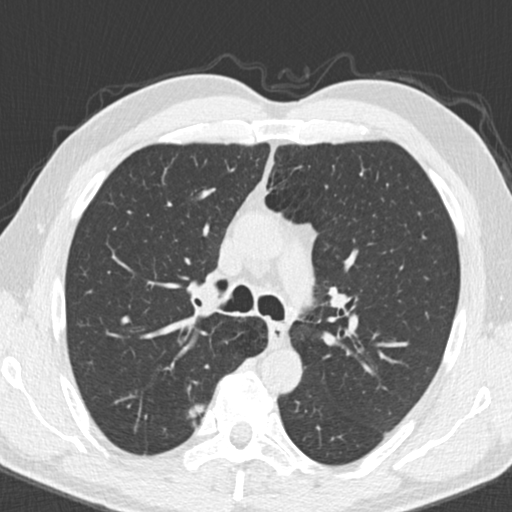
Axial slice from a low-dose chest CT screening exam; third annual screen; lung window (W 1500 / L -600 HU); 2 mm slice thickness; slice 61 of 192 in the series. Male, age 55 years at enrolment. Current smoker at enrolment.
Expert-annotated lung lesion, bounding box (x1, y1, x2, y2) in pixels: (172, 398, 217, 438). Reader record for this screening exam (exam-level; its link to the box is not recorded): non-calcified nodule or mass ≥4 mm, right upper lobe, 9 × 7 mm, smooth margins, soft tissue attenuation, pre-existing on the prior screen: no. Official screen result: positive, other.